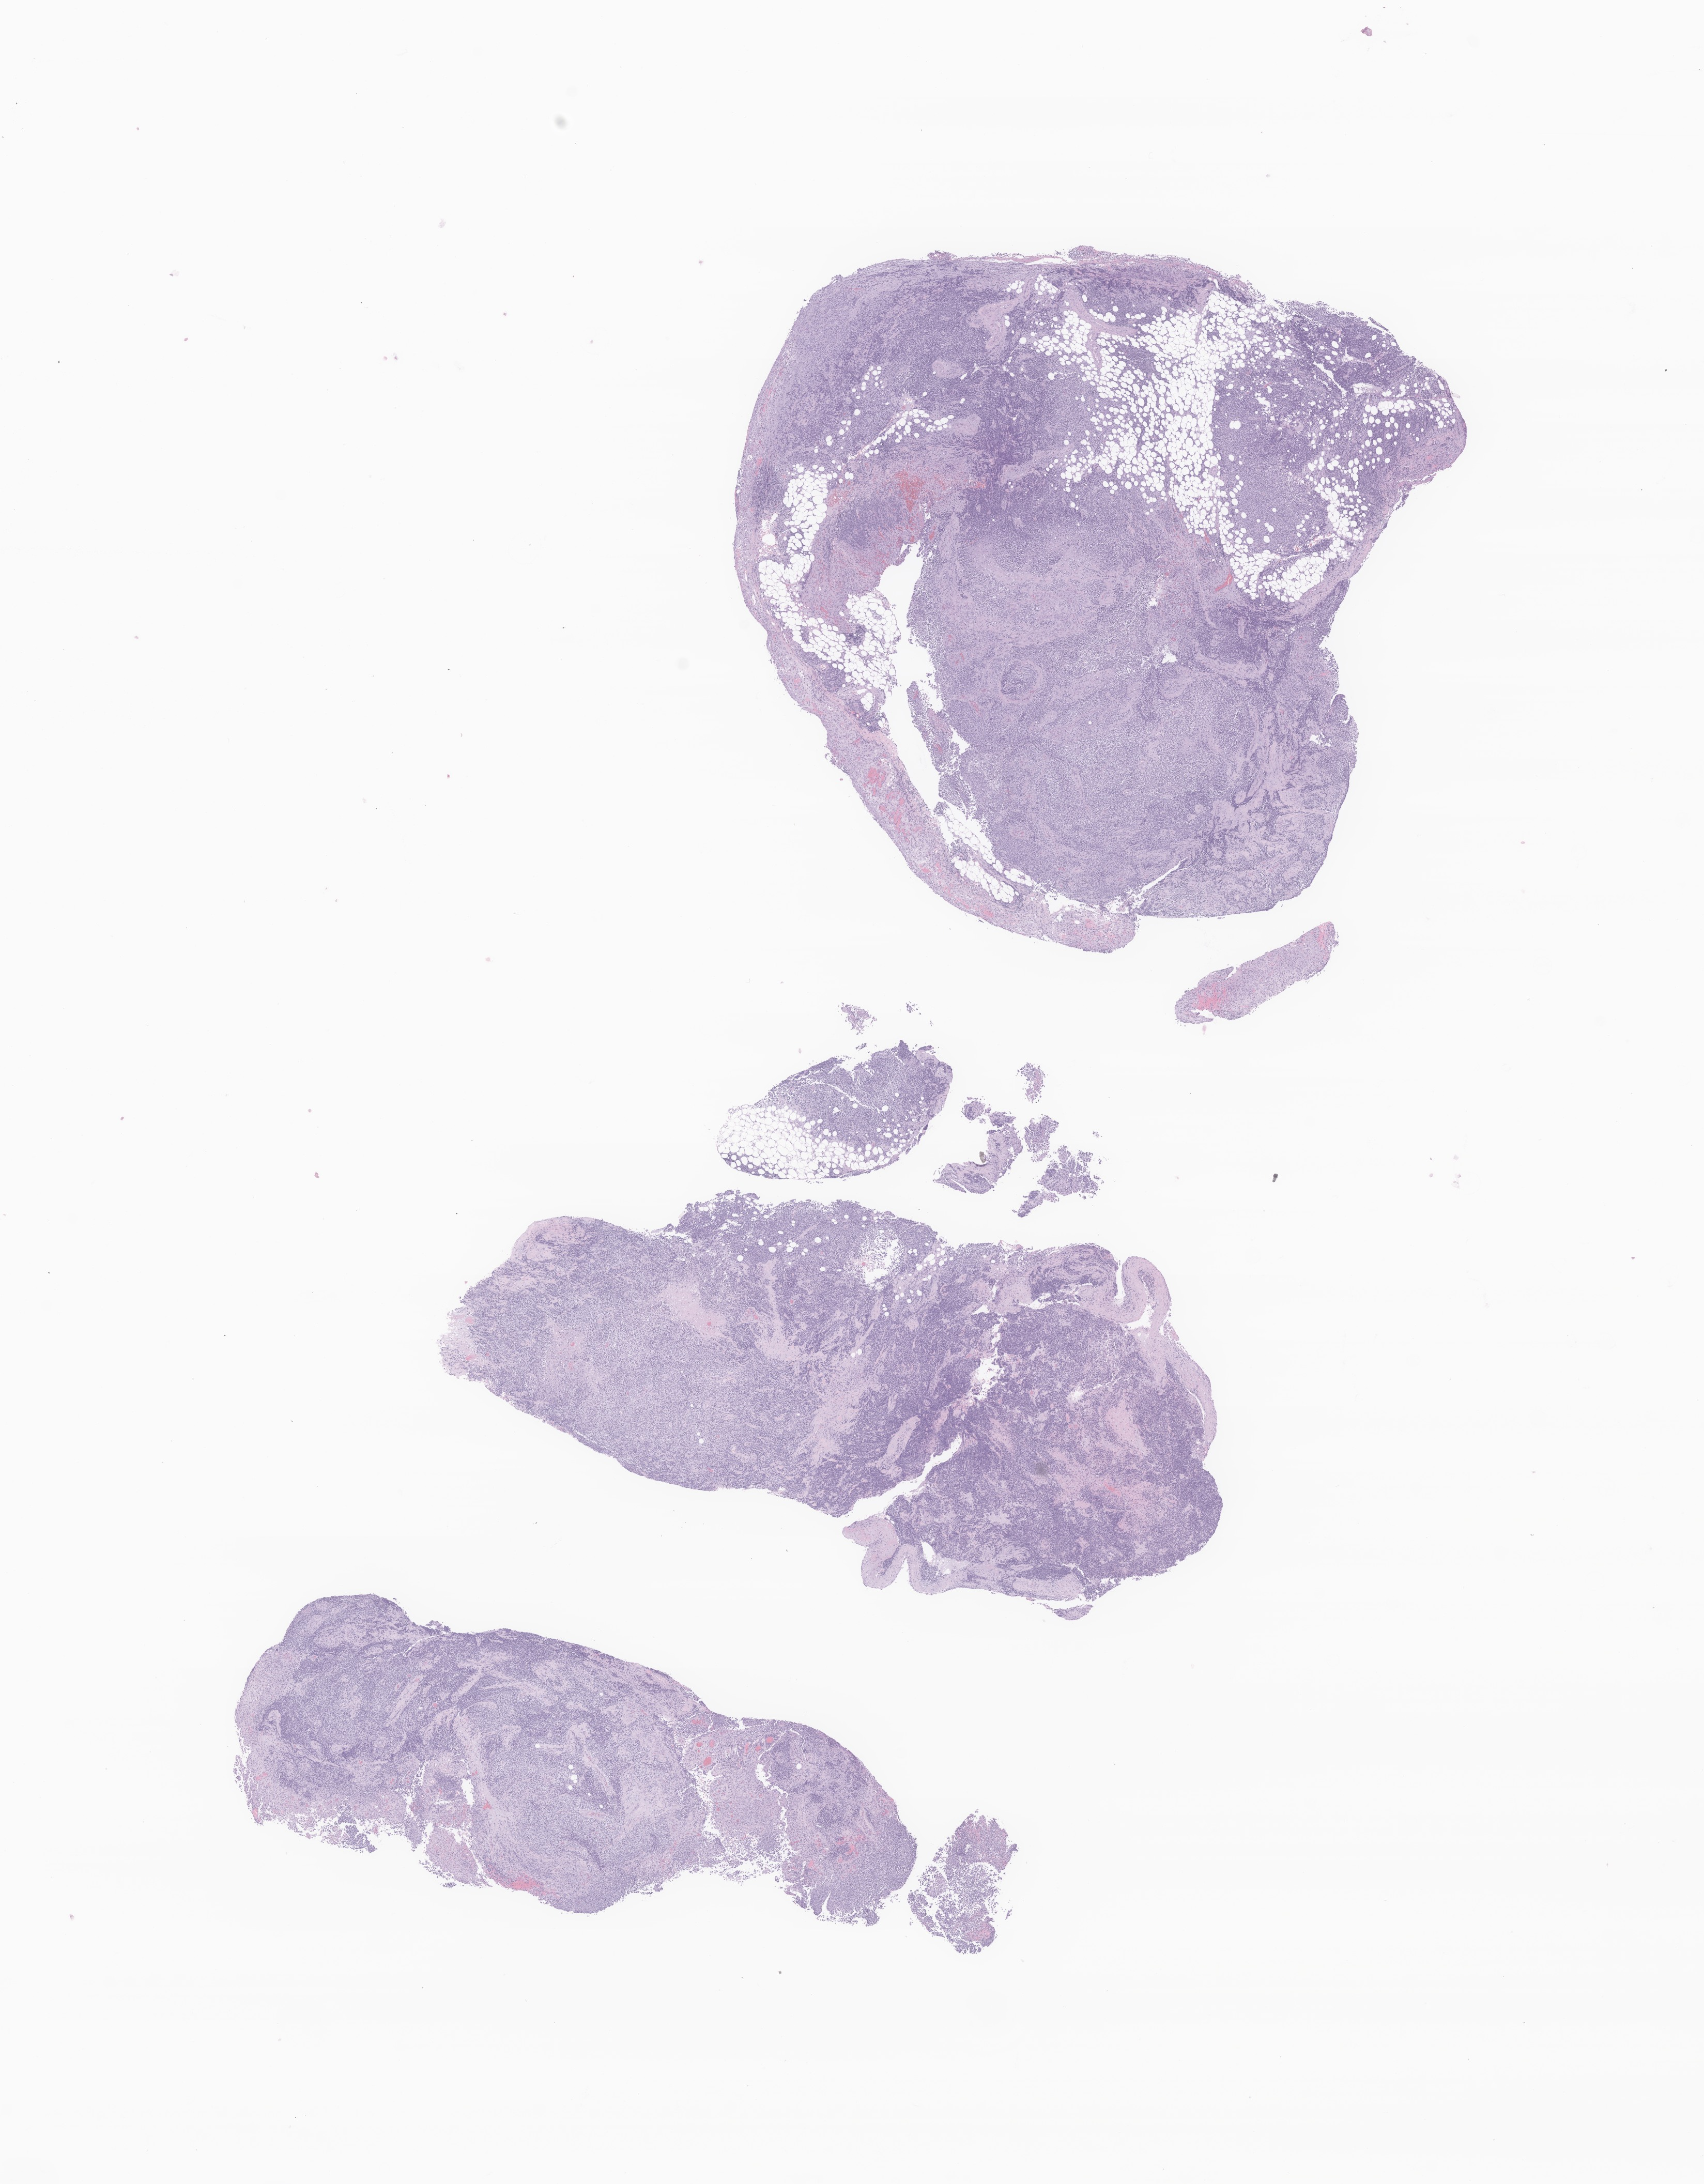
Whole-slide image, H&E stain of tumor tissue from the retroperitoneum, low-resolution overview of the scanned area, about 13.9 x 17.8 mm. FFPE section. Male patient, age 297 months (24 years 9 months).
Diagnosis (ICD-O-3 morphology term): Alveolar rhabdomyosarcoma.